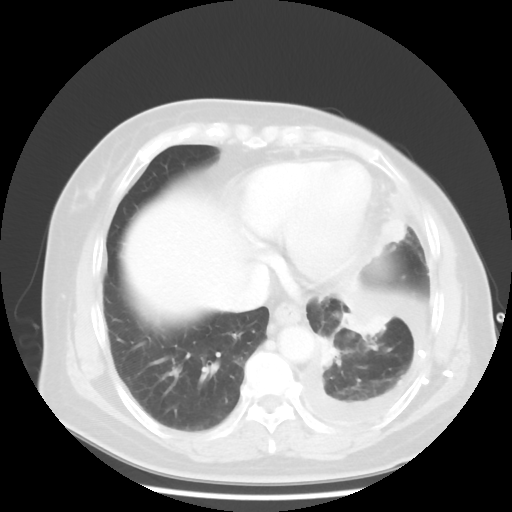
Chest CT, one axial slice. Position 13 of 48 along the scan axis. Reconstruction kernel STANDARD. Lung window (W 1500 / L -600 HU). 512 × 512 image matrix, field of view 360 × 360 mm. Female patient, age 63 years. Case-level facts recorded for this patient, not image findings: clinical TNM (as recorded): T2 N0 M1.
Outlined on this slice (bounding box drawn by a radiologist):
- lung tumour (recorded histology: adenocarcinoma): bounding box (x1, y1, x2, y2) in pixels: (336, 292, 394, 356)